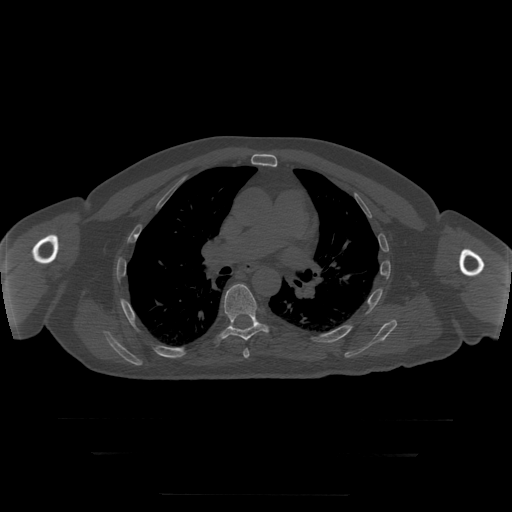
CT including the spine, one axial slice; position 189 of 397 along the scan axis; reconstruction kernel STANDARD; 120 kVp; bone window (W 1800 / L 400 HU); 1.25 mm slice thickness; 512 × 512 image matrix, field of view 510 × 510 mm. Patient age 73 years. From the clinical record (not read from this slice): primary cancer: prostate.
Structures marked on this image (semi-automatically segmented with operator editing):
- T6 vertebra: bounding box (x1, y1, x2, y2) in pixels: (244, 349, 250, 359)
- T7 vertebra: (214, 284, 270, 344)